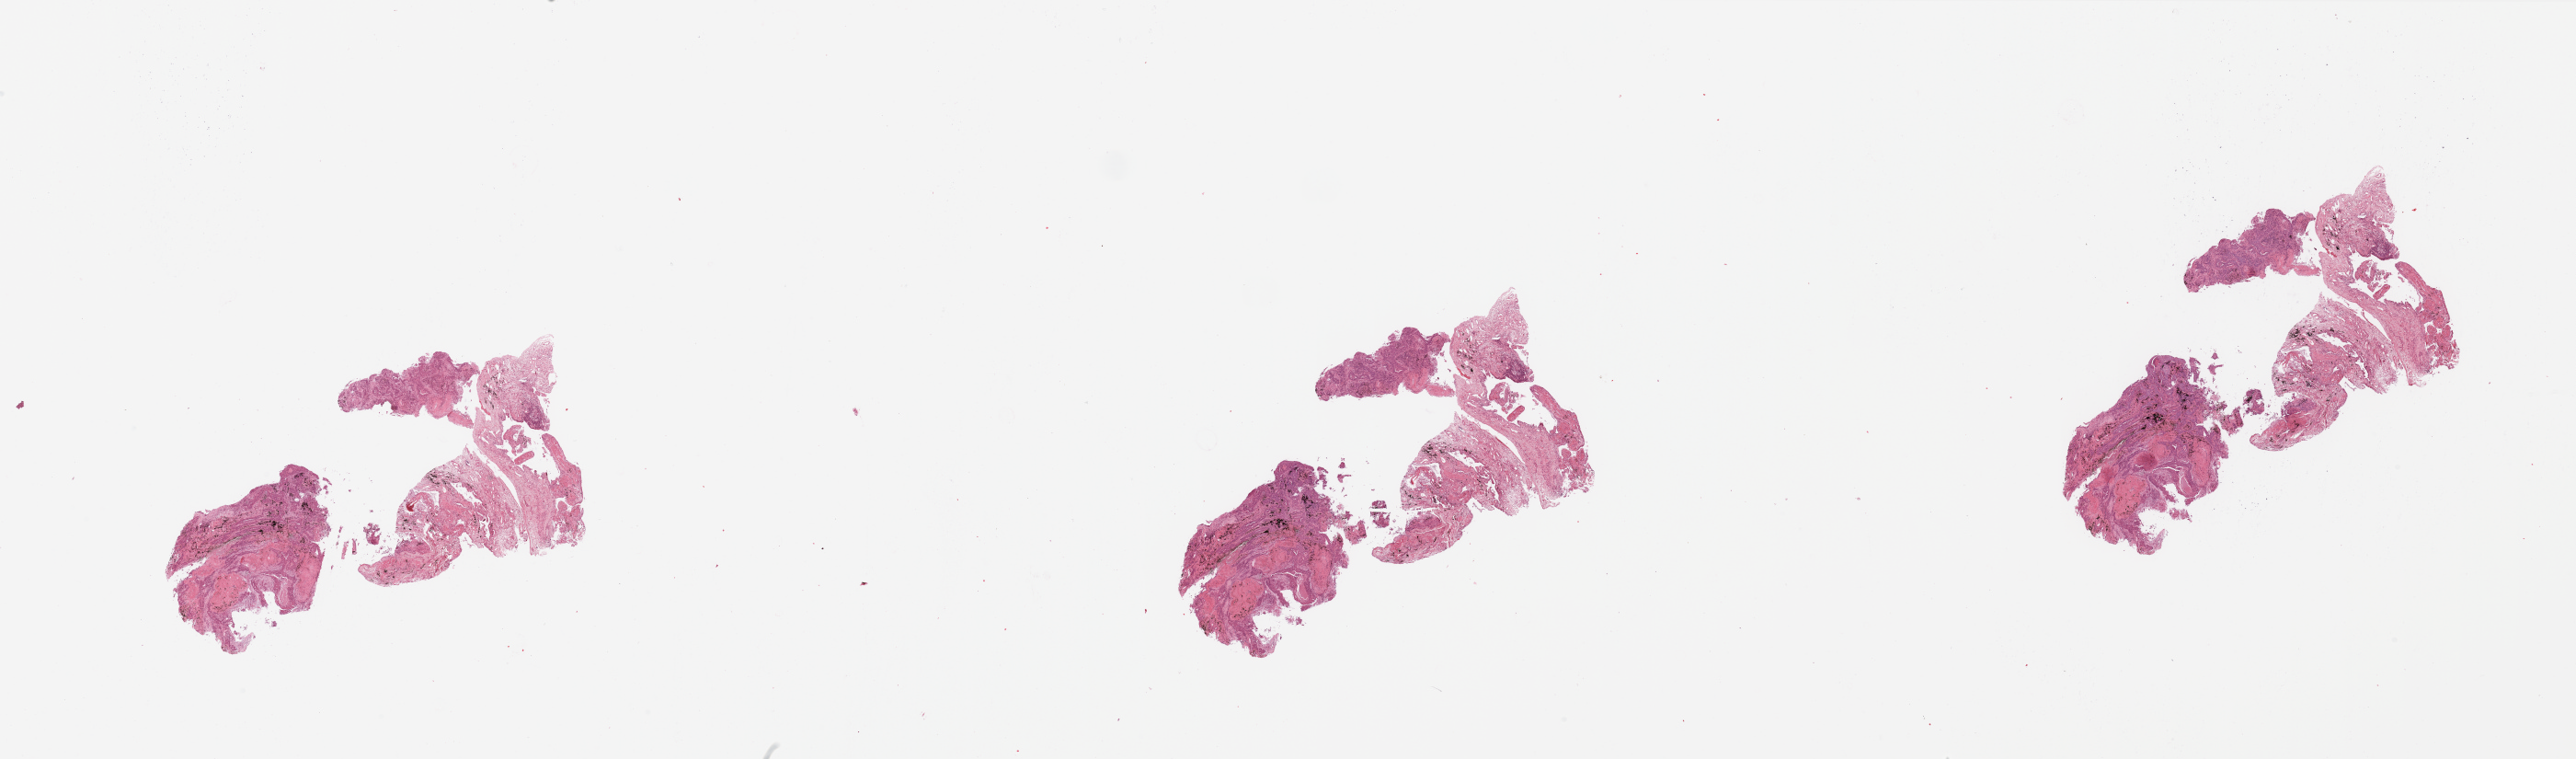
H&E whole-slide image, shown as a low-resolution overview of the whole scanned area (about 44.3 x 13.0 mm, acquisition: 20x scan), tumour tissue sample, sampled site: lung. Male, 73 y/o. Histologic grade: G2 (moderately differentiated). Slide review estimates, as recorded: tumour nuclei 60%, necrosis 2%.
• diagnosis: Squamous cell carcinoma, NOS
• AJCC pathologic stage: IIA
• primary tumour site (as recorded): right upper lobe